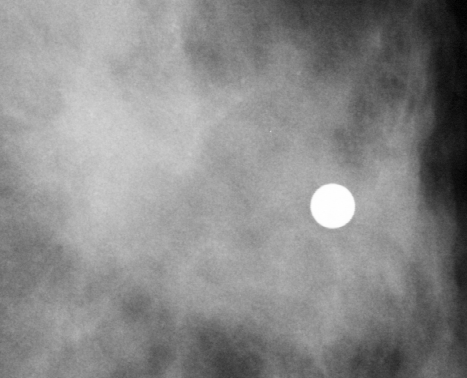
Region of interest cut from a scanned film mammogram (one marked finding); left breast; CC view.
Marked abnormality: mass, shape irregular, margins spiculated; BI-RADS assessment category 4; subtlety rating 5 on a 1 (subtle) to 5 (obvious) scale; pathology (as recorded): malignant.